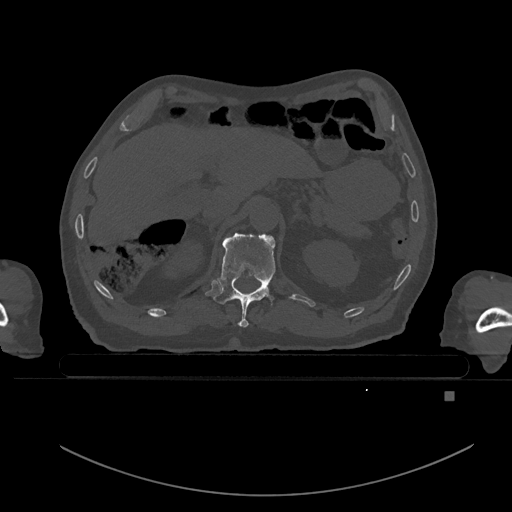
CT including the spine, one axial slice; slice 25 of 969 in the series (ordered by position); bone window (W 1800 / L 400 HU); 0.5 mm slice thickness; 512 × 512 image matrix, field of view 456 × 456 mm. Male patient, age 82 years. Case-level facts recorded for this patient, not image findings: primary cancer: prostate; vertebrae with lytic lesions (as recorded): T11, T9, T8, T2.
Outlined on this slice (semi-automatically segmented with operator editing):
- T11 vertebra: bounding box (x1, y1, x2, y2) in pixels: (213, 233, 275, 327)